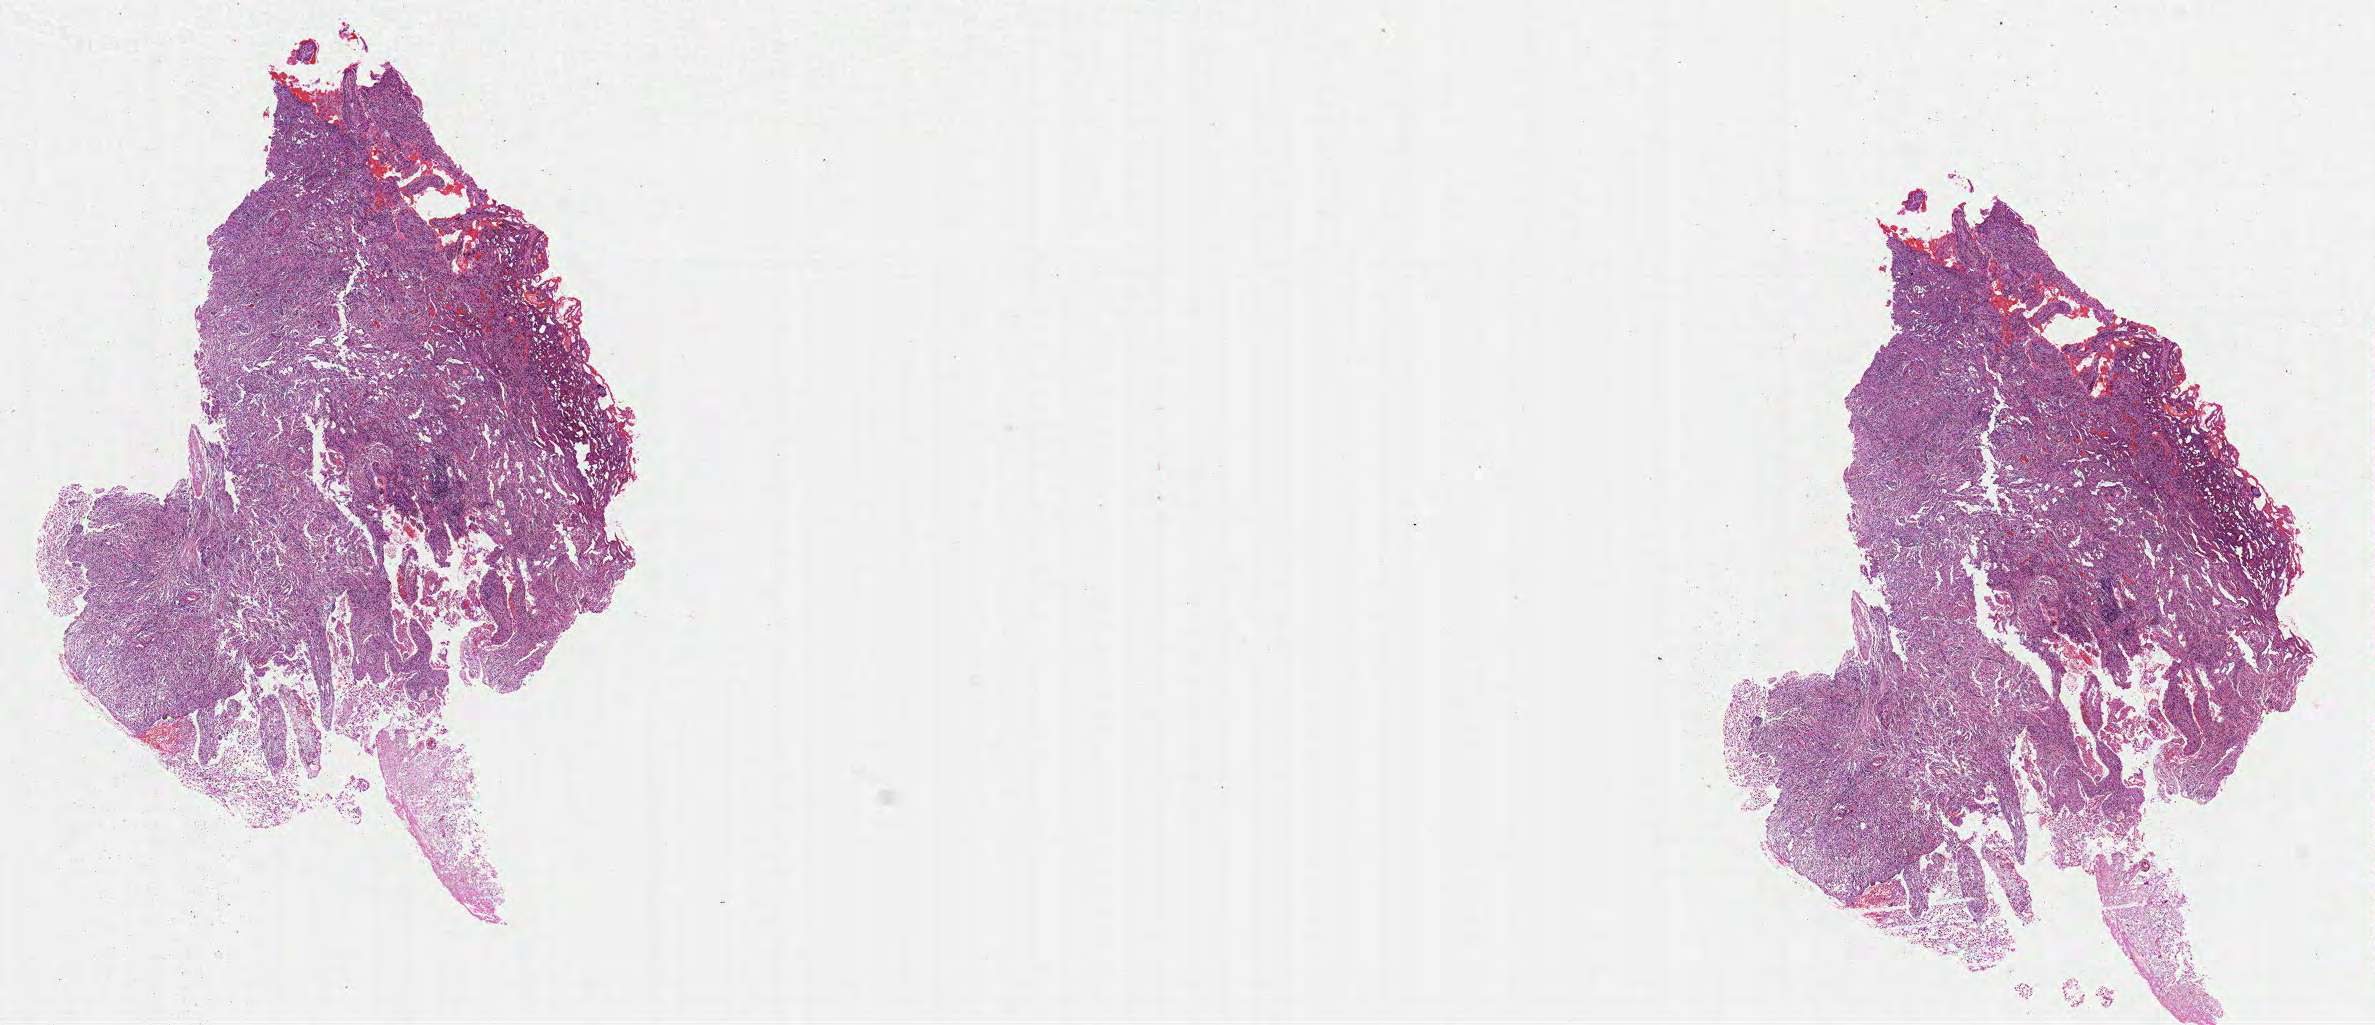
Digitized Hematoxylin and eosin (H&E) stained tissue section (whole slide), whole scanned area (about 19.0 x 8.2 mm, from a 20x scan) shown as a low-resolution overview; FFPE section; brain, primary tumour sample. Patient: female, age at initial diagnosis 48 years.
Histologic diagnosis: Glioblastoma.